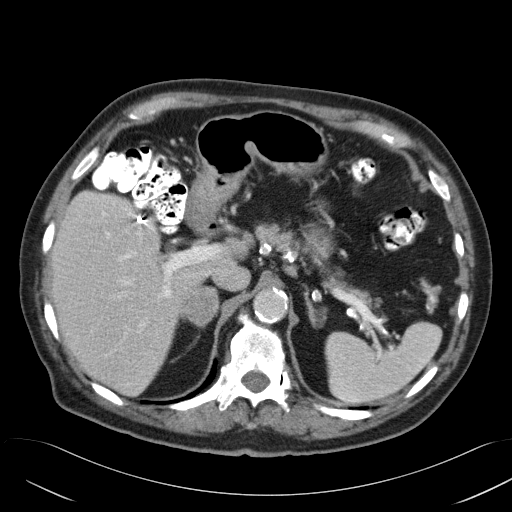
Contrast-enhanced abdominal CT, one axial slice; slice 35 of 58 in the series (ordered by position); reconstruction kernel B31f; 120 kVp; intravenous contrast given; soft-tissue window (W 400 / L 40 HU); 5 mm slice thickness; 512 × 512 image matrix, field of view 384 × 384 mm. Male patient, age 82 years. Case-level facts recorded for this patient, not image findings: diagnosis: adrenocortical carcinoma; tumour side: right adrenal; tumour size at pathology: 9 cm; Ki-67 index: 30 %; stage (as recorded): 3.
Annotated regions visible in this slice (semi-automatic segmentation, software-assisted and operator-edited):
- mass: box from (x=181, y=288) to (x=221, y=323) px